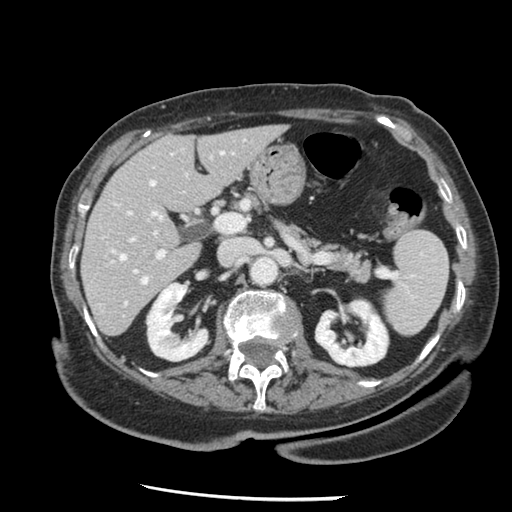
Contrast-enhanced abdominal CT, one axial slice; slice 72 of 148 in the series (ordered by position); reconstruction kernel STANDARD; 120 kVp; intravenous contrast given; soft-tissue window (W 400 / L 40 HU); 2.5 mm slice thickness; 512 × 512 image matrix. Female patient, age 85 years. Case-level facts recorded for this patient, not image findings: diagnosis: colorectal cancer liver metastases, imaged before liver resection; multiple liver metastases: no; largest metastasis: 0.9 cm; disease in both lobes: no.
Annotated regions visible in this slice (outlined manually by an expert reader):
- hepatic veins: bounding box (x1, y1, x2, y2) in pixels: (112, 149, 183, 304)
- liver: (83, 126, 284, 335)
- planned liver remnant (the part of the liver to remain after resection): (83, 126, 284, 335)
- portal vein (with intrahepatic branches): (127, 150, 226, 274)